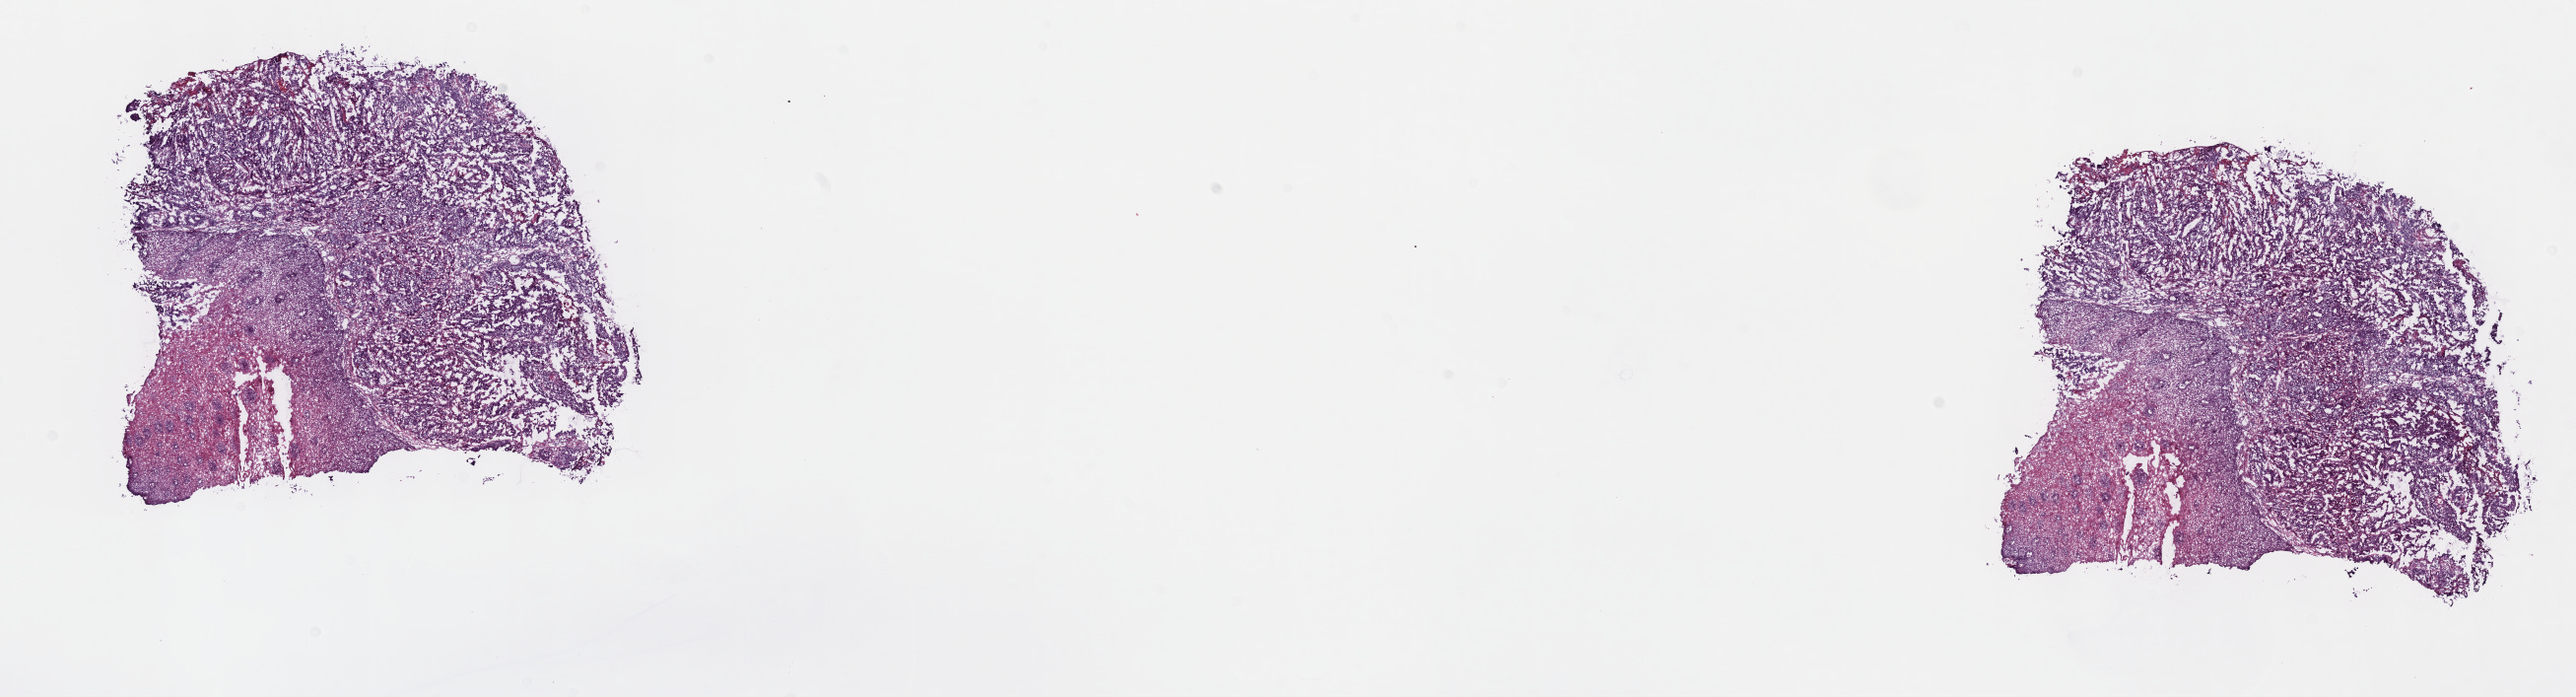
H&E-stained whole-slide image, shown as a low-resolution overview of the whole scanned area (about 21.1 x 5.7 mm, from a 40x scan); frozen section from the top of the tissue portion; primary tumour sample from the esophagus. Male patient; age at initial diagnosis 53 years. Histologic grade: G2 (moderately differentiated). Slide review estimates, as recorded: tumour cells 55%, tumour nuclei 70%, normal cells 0%, stromal cells 35%, necrosis 10%. Inflammatory infiltration, as recorded: lymphocyte infiltration 1%, monocyte infiltration 1%, neutrophil infiltration 0%.
TNM: T1 N1 M0. AJCC pathologic stage: IIB. Histologic diagnosis: Adenocarcinoma, NOS (lower third of esophagus).